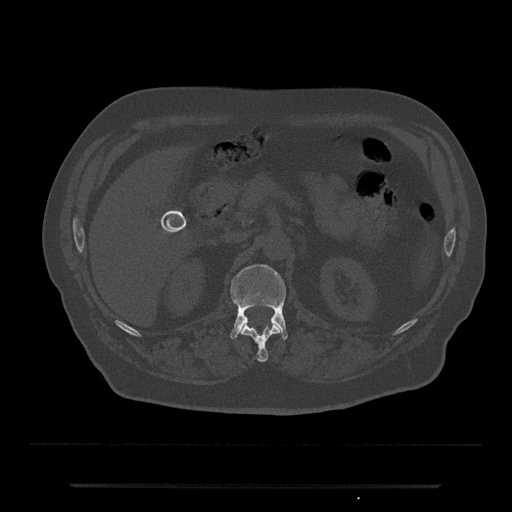
CT including the spine, one axial slice; position 558 of 797 along the scan axis; reconstruction kernel Br40s/3; 120 kVp; bone window (W 1800 / L 400 HU); 0.5 mm slice thickness; 512 × 512 image matrix, field of view 434 × 434 mm. Male patient, age 80 years. From the clinical record (not read from this slice): primary cancer: prostate.
Outlined on this slice (semi-automatic segmentation, software-assisted and operator-edited):
- L1 vertebra: bounding box [x1, y1, x2, y2] px = [230, 265, 288, 339]
- T12 vertebra: [242, 324, 280, 362]